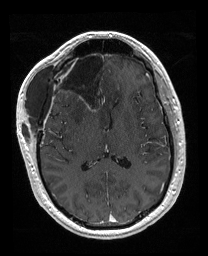
Brain MRI from a brain-tumour surgery series, one axial slice. T1-weighted post-contrast. 1 mm slice thickness. 208 × 256 image matrix. Case-level facts recorded for this patient, not image findings: histopathology: Astrocytoma; WHO grade: 4; IDH mutation: yes; tumour location: Right Orbitofrontal Anterior Temporal Insular.
Annotated regions visible in this slice (manually delineated by an expert):
- previous resection cavity: bounding box <56,52,106,111> (left, top, right, bottom; pixels)